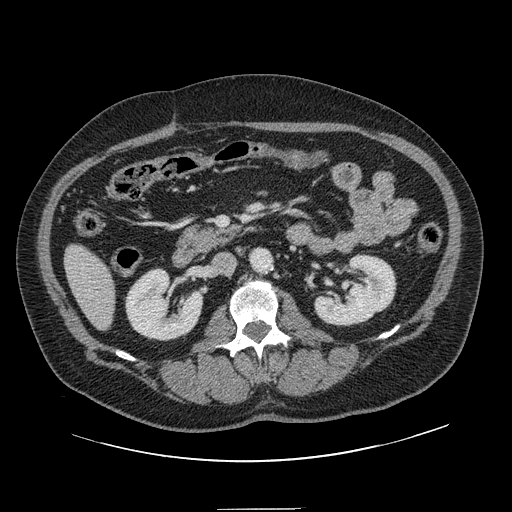
Contrast-enhanced abdominal CT, one axial slice. Position 44 of 154 along the scan axis. 120 kVp. Intravenous contrast given. Soft-tissue window (W 400 / L 40 HU). 2.5 mm slice thickness. 512 × 512 image matrix, field of view 451 × 451 mm. Male patient, age 61 years. Case-level facts recorded for this patient, not image findings: diagnosis: colorectal cancer liver metastases, imaged before liver resection; multiple liver metastases: yes; largest metastasis: 2.6 cm; disease in both lobes: yes.
Annotated regions visible in this slice (manually delineated by an expert):
- liver: bounding box [x1, y1, x2, y2] px = [66, 246, 115, 328]
- planned liver remnant (the part of the liver to remain after resection): [66, 246, 115, 329]